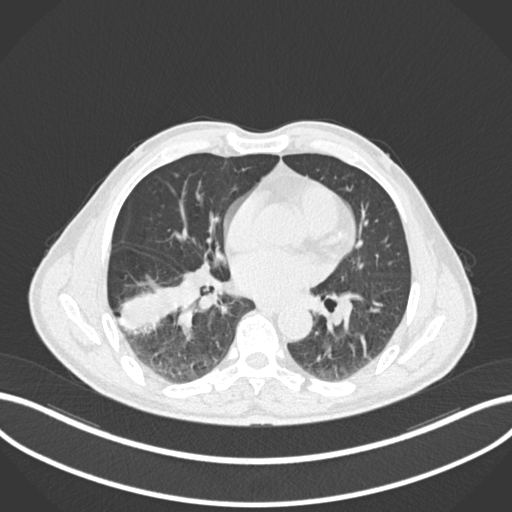
Chest CT, one axial slice; lung window (W 1500 / L -600 HU); 1 mm slice thickness; 512 × 512 image matrix, field of view 400 × 400 mm. Patient: male, 58 years. From the clinical record (not read from this slice): clinical TNM (as recorded): T3 N0 M0; histopathological grade: G2.
Structures marked on this image (rectangle marked by the reading radiologist):
- lung tumour (recorded histology: squamous cell carcinoma): bounding box <119,277,176,334> (left, top, right, bottom; pixels)